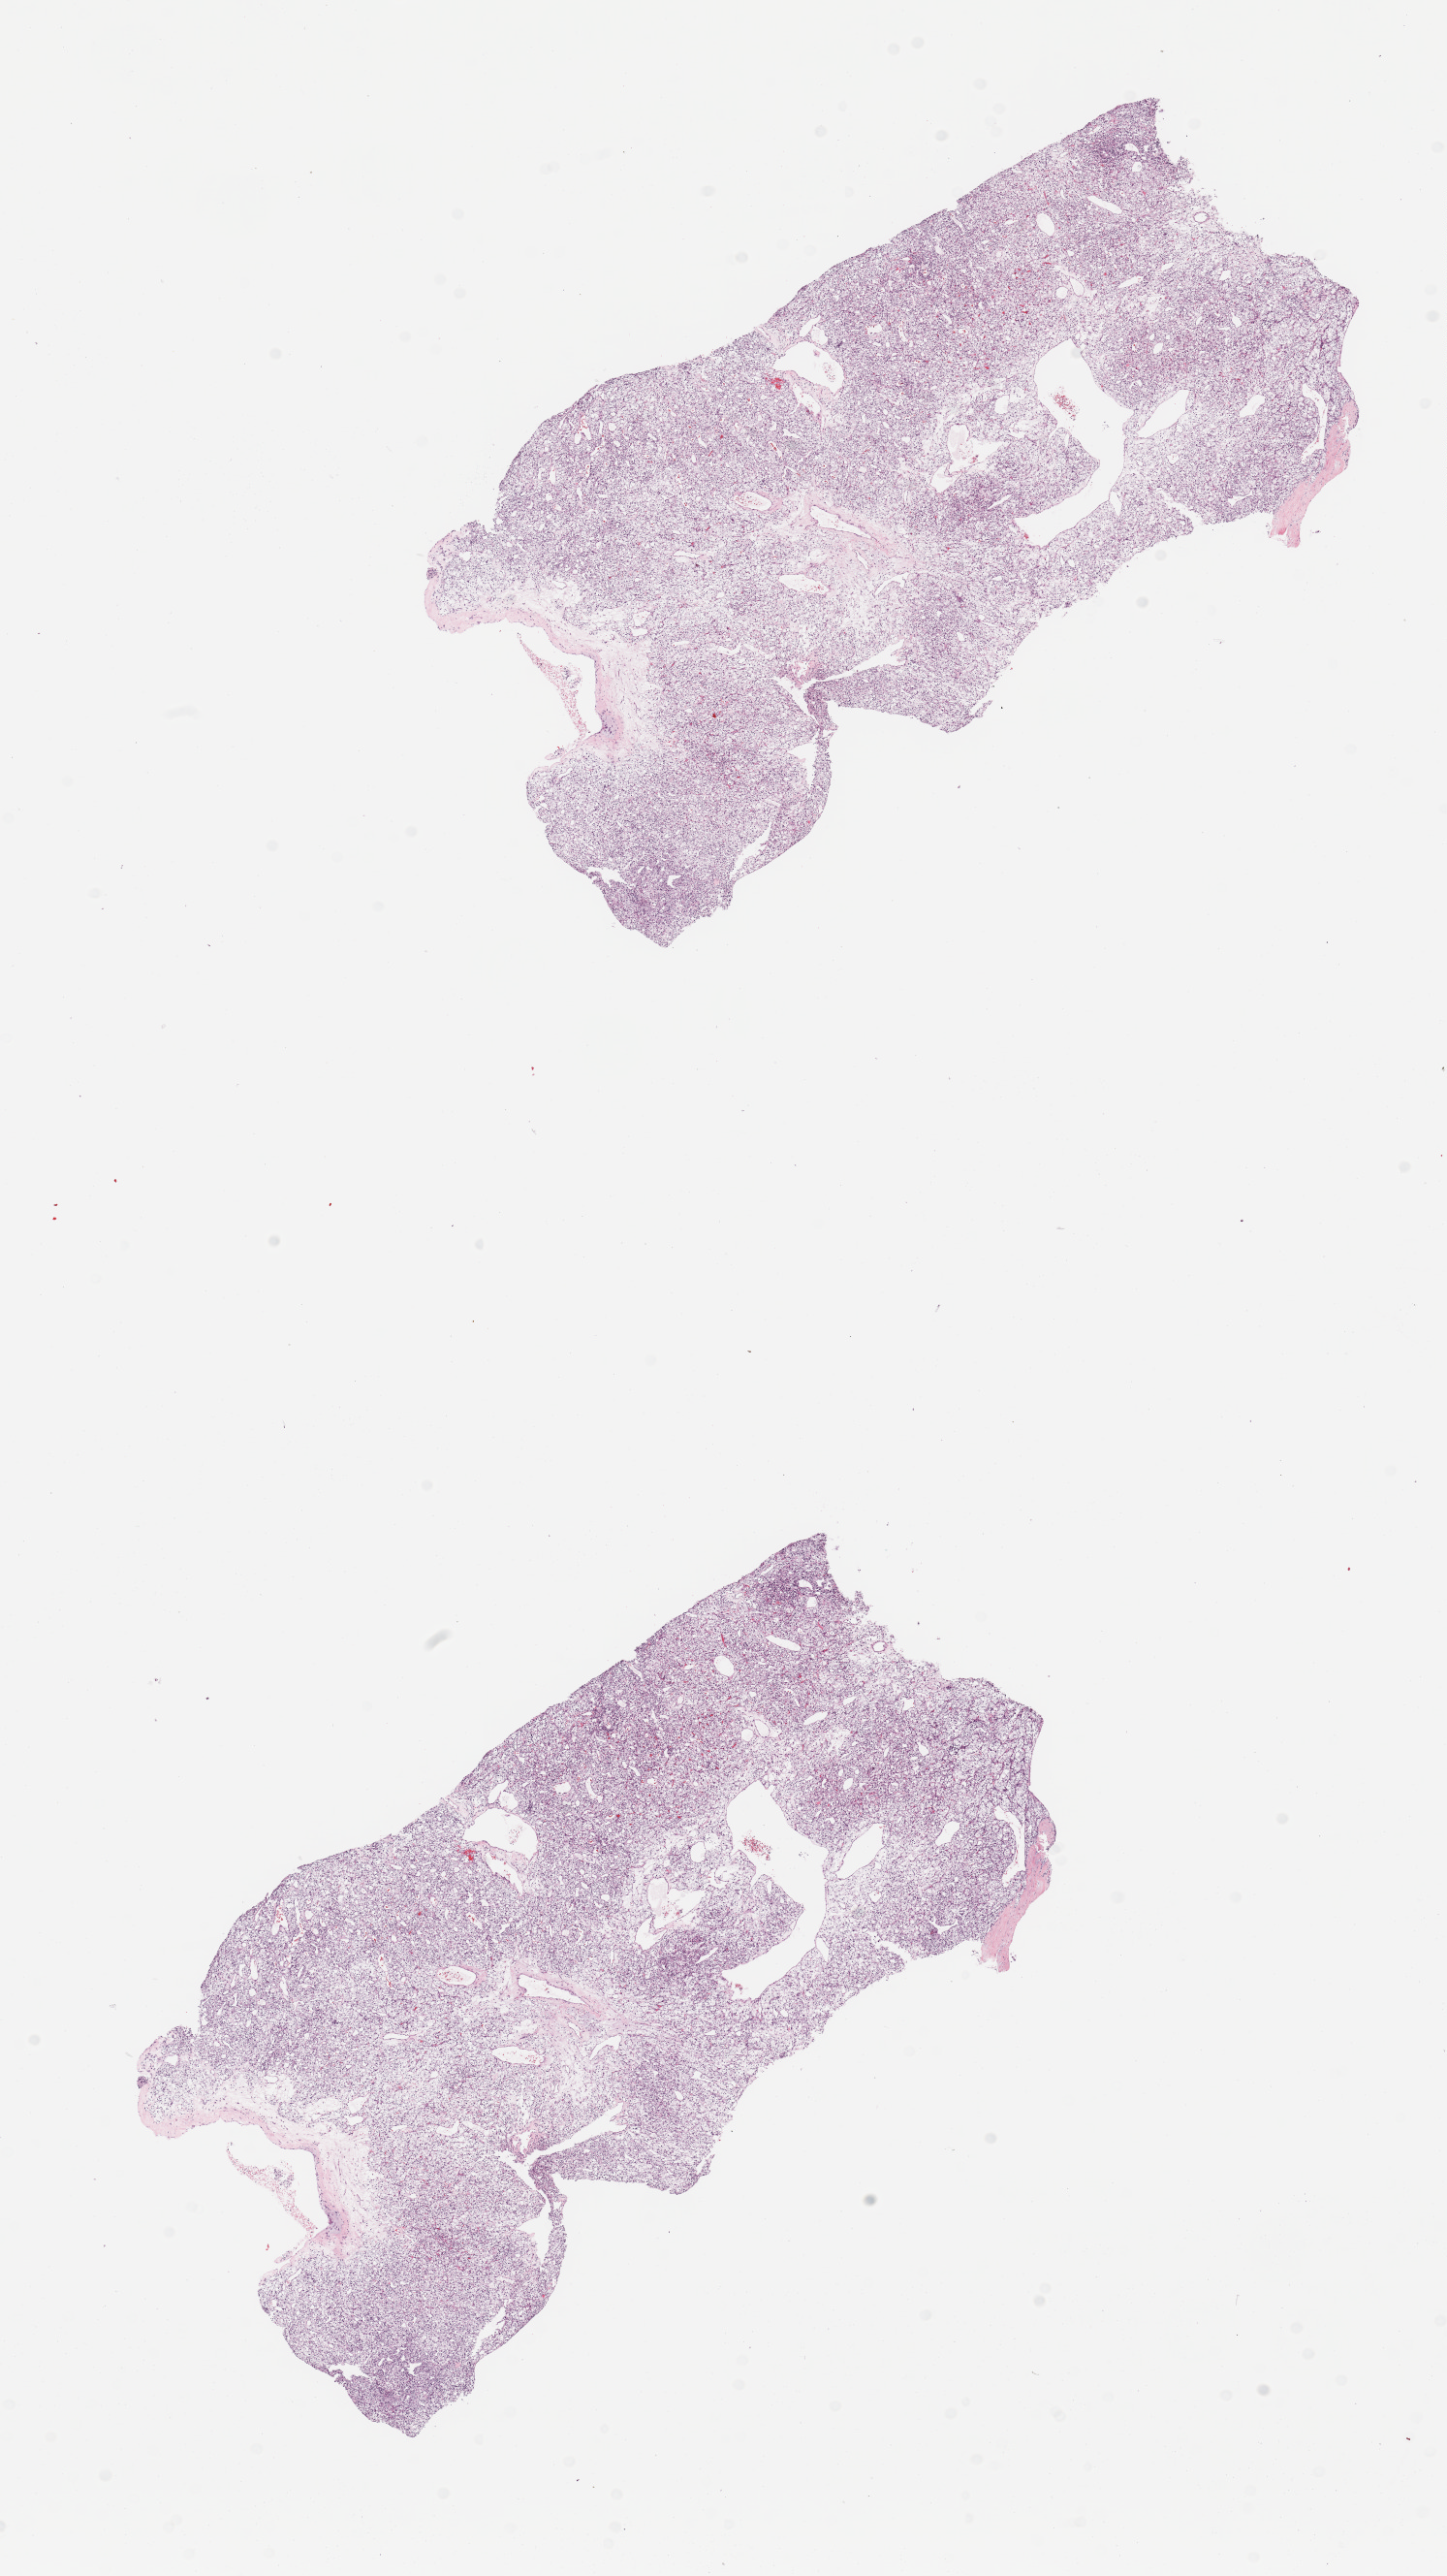
H&E-stained whole-slide image — low-resolution overview of the scanned area, about 11.8 x 21.0 mm; tumour tissue sample, sampled site: kidney. 56-year-old male patient. Histologic grade: G3 (poorly differentiated). Pathologist review of this section (percent, as recorded): tumour nuclei 90%, necrosis 0%.
Histologic diagnosis: Renal cell carcinoma, NOS. AJCC pathologic stage: III. Primary tumour site (as recorded): middle.